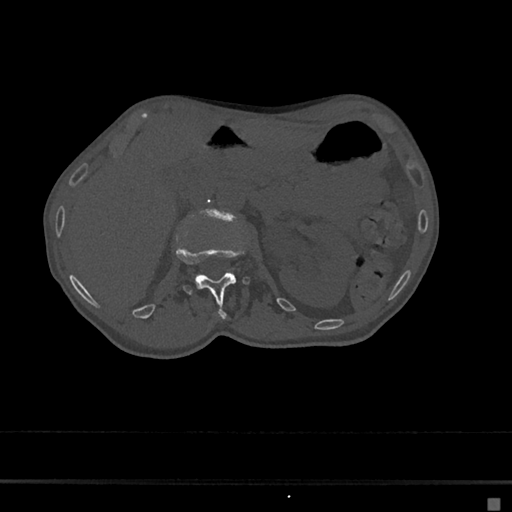
CT including the spine, one axial slice; position 62 of 797 along the scan axis; reconstruction kernel Br40s/3; bone window (W 1800 / L 400 HU); 512 × 512 image matrix, field of view 360 × 360 mm. Female patient, age 68 years. Case-level facts recorded for this patient, not image findings: primary cancer: renal.
Annotated regions visible in this slice (semi-automatically segmented with operator editing):
- L1 vertebra: bounding box (x1, y1, x2, y2) in pixels: (174, 243, 251, 318)
- L2 vertebra: (205, 210, 232, 218)